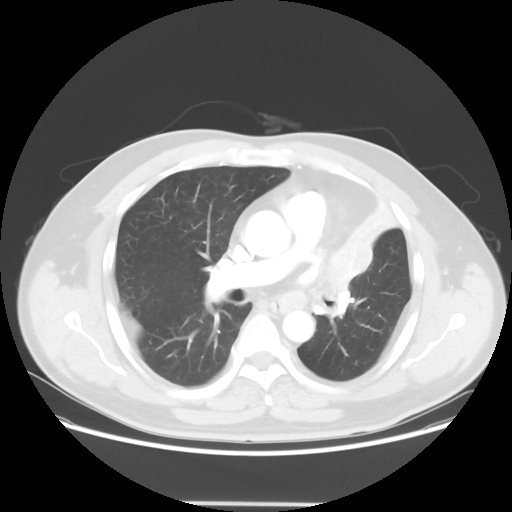
Chest CT, one axial slice; slice 36 of 62 in the series (ordered by position); lung window (W 1500 / L -600 HU); 5 mm slice thickness; 512 × 512 image matrix, field of view 403 × 403 mm. Male patient, age 49 years. Case-level facts recorded for this patient, not image findings: clinical TNM (as recorded): T3 N3 M1c.
Structures marked on this image (bounding box drawn by a radiologist):
- lung tumour (recorded histology: squamous cell carcinoma): box from (x=316, y=239) to (x=364, y=325) px